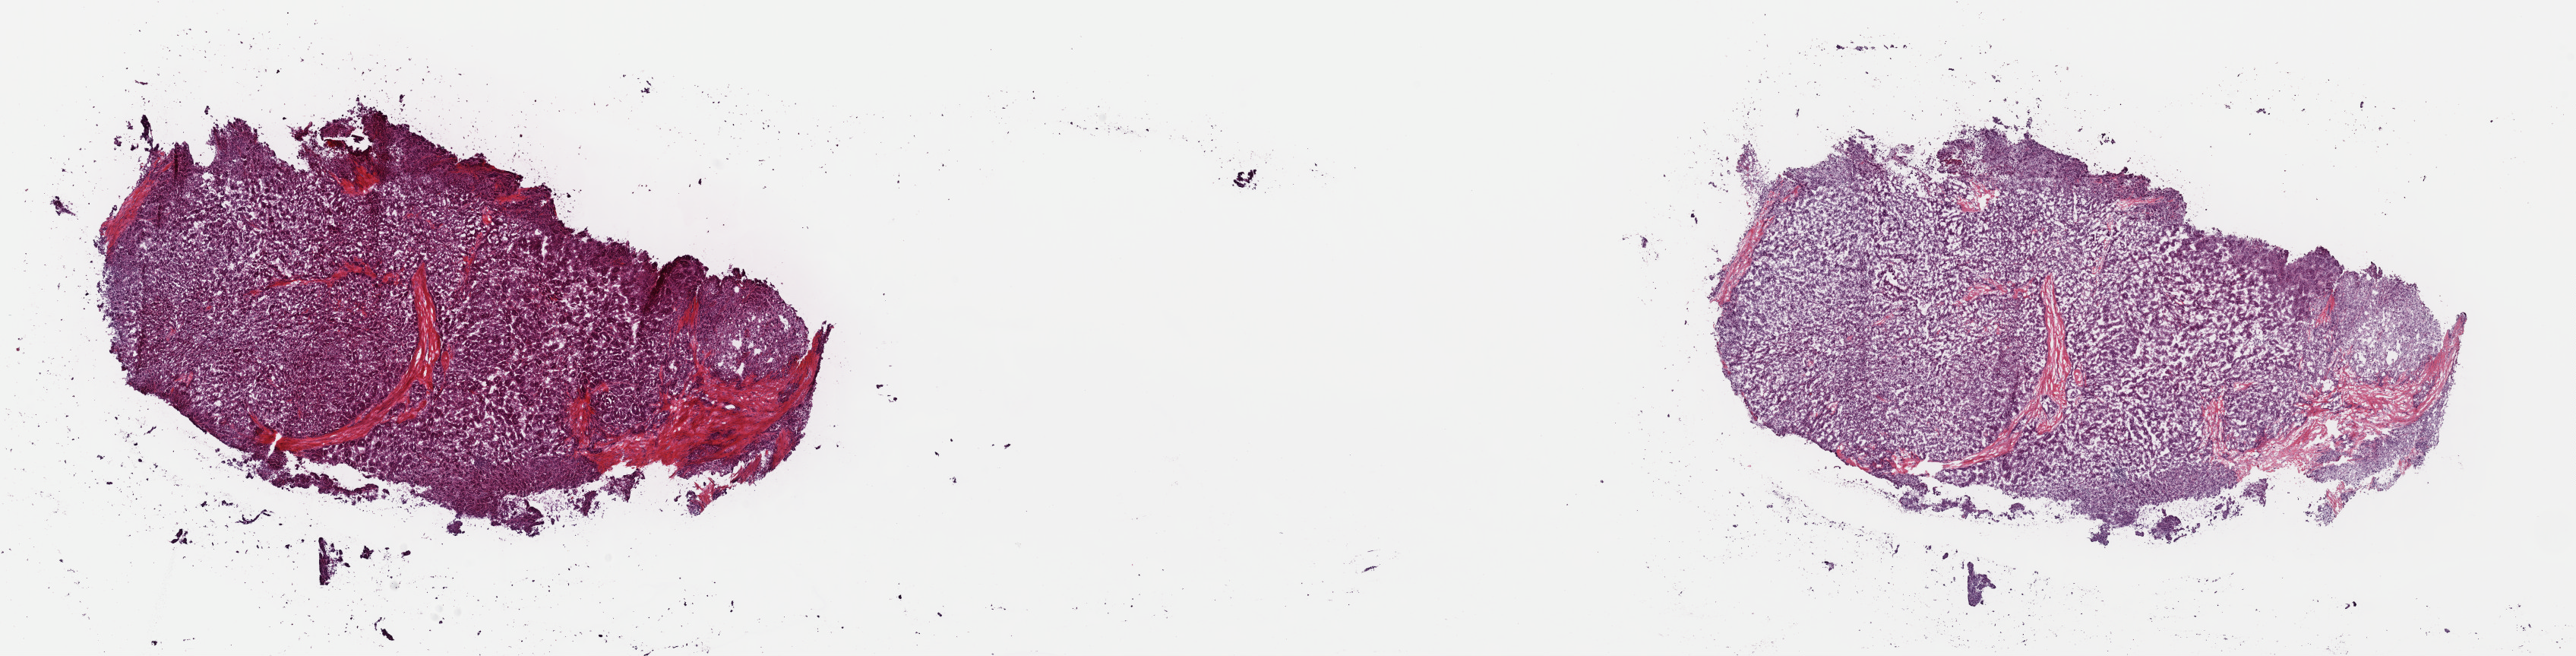
H&E whole-slide image, shown as a low-resolution overview of the whole scanned area (about 26.8 x 6.8 mm, acquisition: 40x scan); frozen section from the top of the tissue portion; primary tumour sample from the liver. Male patient; age at initial diagnosis 80 years. Histologic grade: G2 (moderately differentiated). Composition of this section per pathologist review: tumour cells 98%, tumour nuclei 95%, normal cells 0%, stromal cells 2%, necrosis 0%. Inflammatory infiltration, as recorded: lymphocyte infiltration 0%, monocyte infiltration 0%, neutrophil infiltration 0%.
Histologic diagnosis: Hepatocellular carcinoma, NOS. AJCC pathologic stage: I (7th edition).